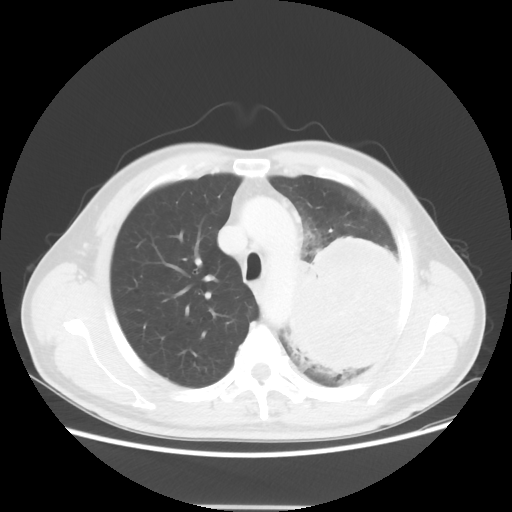
Chest CT, one axial slice; position 40 of 53 along the scan axis; 100 kVp; lung window (W 1500 / L -600 HU); 5 mm slice thickness; 512 × 512 image matrix, field of view 391 × 391 mm. Patient: male, 60 years. From the clinical record (not read from this slice): clinical TNM (as recorded): T4 N1 M1a.
Outlined on this slice (rectangle marked by the reading radiologist):
- lung tumour (recorded histology: large cell carcinoma): box from (x=288, y=234) to (x=404, y=392) px